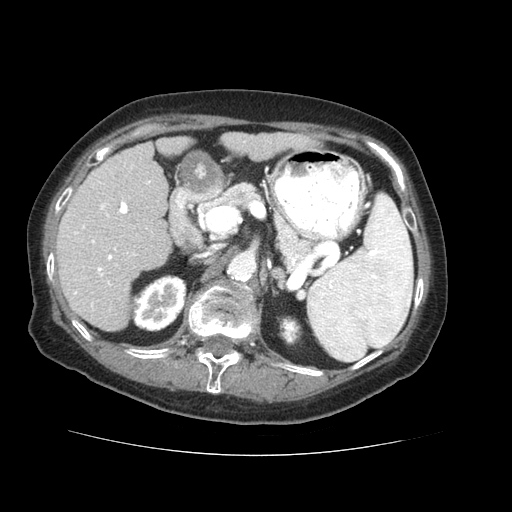
Contrast-enhanced abdominal CT (liver protocol), one axial slice; position 27 of 73 along the scan axis; reconstruction kernel STANDARD; 120 kVp; soft-tissue window (W 400 / L 40 HU); 512 × 512 image matrix, field of view 360 × 360 mm. Case-level facts recorded for this patient, not image findings: diagnosis: hepatocellular carcinoma (patient treated with transarterial chemoembolisation; whether this scan precedes or follows treatment is not stated here); TNM stage (as recorded): Stage-IVB; Child-Pugh class: A; tumour differentiation: well differentiated; tumour nodularity: uninodular.
Annotated regions visible in this slice (semi-automatic segmentation, software-assisted and operator-edited):
- liver parenchyma outside the tumour (the mass and vessels are separate outlines, so this box may not span the whole liver): bounding box <56,132,316,330> (left, top, right, bottom; pixels)
- liver vessels: <74,141,245,307>